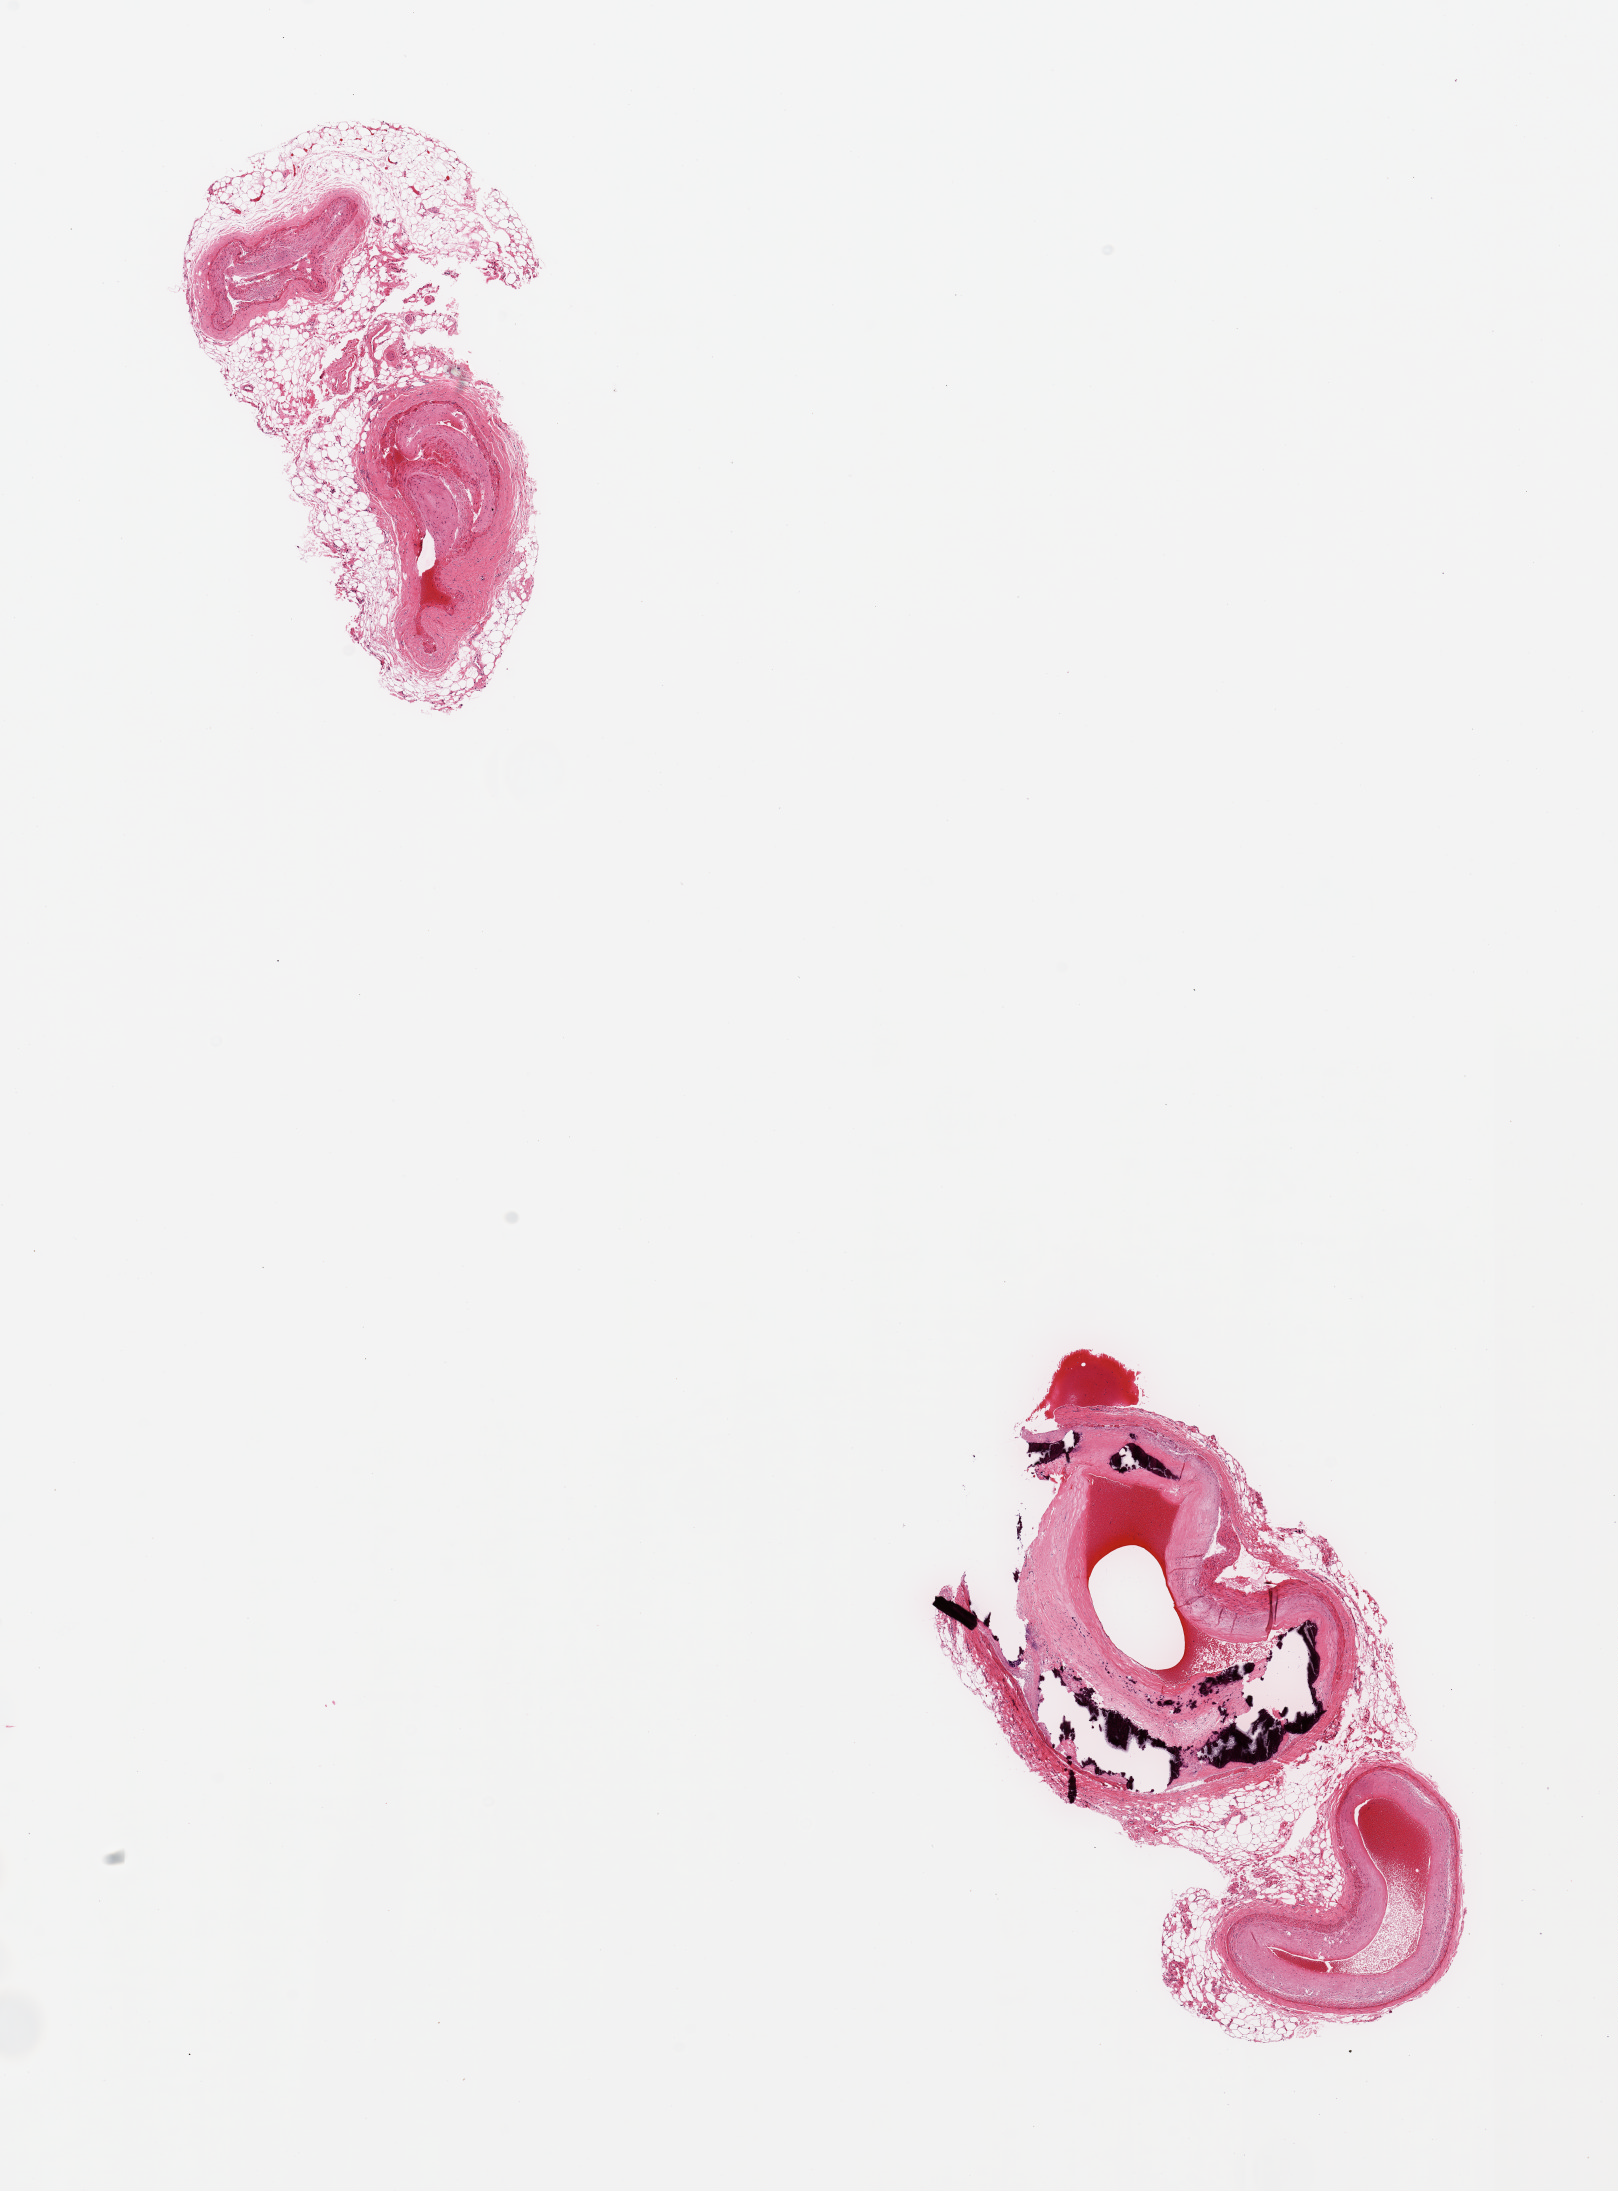
Whole-slide image, haematoxylin and eosin stain, brightfield, a low-resolution overview of the entire scanned area, about 12.8 x 17.3 mm (acquisition: 20x scan). PAXgene-fixed paraffin-embedded (PFPE) section. Sampled site (target tissue): coronary artery. Donor tissue sample. Donor sex: male.
Review note (as recorded): 2 pieces, bifurcation area sampled, beware fat, ~25% of specimen; Subtotally occlusive calcifying atherosis.